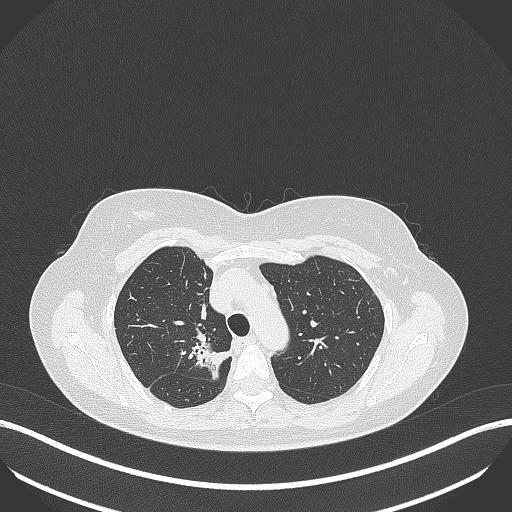
Chest CT, one axial slice. Slice 293 of 386 in the series (ordered by position). Lung window (W 1500 / L -600 HU). 1 mm slice thickness. 512 × 512 image matrix. Female patient, age 65 years. From the clinical record (not read from this slice): clinical TNM (as recorded): T1b N0 M0.
Outlined on this slice (bounding box drawn by a radiologist):
- lung tumour (recorded histology: adenocarcinoma): bounding box (x1, y1, x2, y2) in pixels: (190, 336, 230, 381)